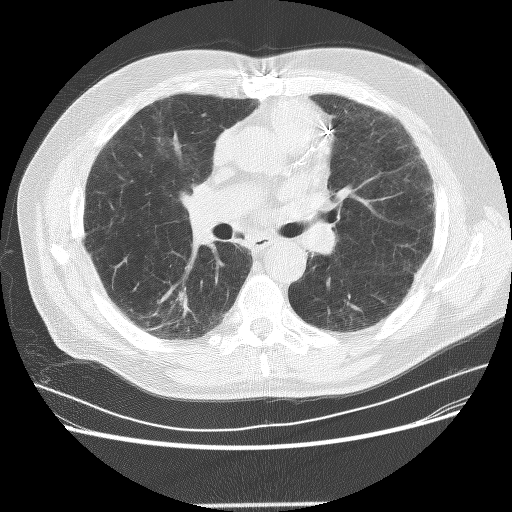
Low-dose screening chest CT, axial slice, baseline annual screen, lung window (W 1500 / L -600 HU), lung (sharp) reconstruction kernel (BONE), slice 121 of 281 in the series, 512 × 512 image matrix. Male participant, aged 72 years at enrolment. Former smoker at enrolment.
• Expert-annotated lung lesion, bounding box (x1, y1, x2, y2) in pixels: (162, 282, 201, 322).
• The screening reader recorded 2 non-calcified nodules or masses ≥4 mm on this exam (right lower lobe, left lower lobe); which of them this box marks is not recorded.
• Official screen result: positive, change unspecified: nodule(s) >= 4 mm or enlarging nodule(s), mass(es), or other non-specific abnormalities suspicious for lung cancer.
• Participant outcome: lung cancer diagnosed 436 days after this screen (after the second annual screen) — squamous cell carcinoma, NOS, right lower lobe, poorly differentiated (G3), stage IB (AJCC 6th edition), 42 mm at pathology.